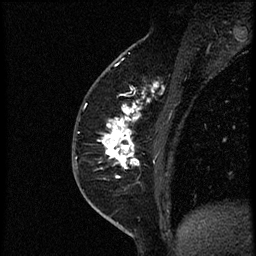
Breast MRI (dynamic contrast-enhanced), one sagittal slice; position 25 of 56 along the scan axis; dynamic contrast-enhanced study with each time point stored as its own series, time point 2 of 4 at this slice position (early post-contrast, ordered by acquisition time); 1.5 T; TE 4.2 ms, TR 18.9 ms; 2 mm slice thickness; 256 × 256 image matrix. Female patient. From the clinical record (not read from this slice): setting: breast cancer imaged before/during neoadjuvant chemotherapy; receptor status: HER2-positive.
Annotated regions visible in this slice (semi-automatically segmented with operator editing):
- analysis volume of interest (the breast-tissue region the enhancement analysis was run in; not a lesion): bounding box <96,85,174,189> (left, top, right, bottom; pixels)
- tumour enhancement mask (voxels above the 100 % enhancement threshold inside the analysis volume of interest): <99,88,156,177>